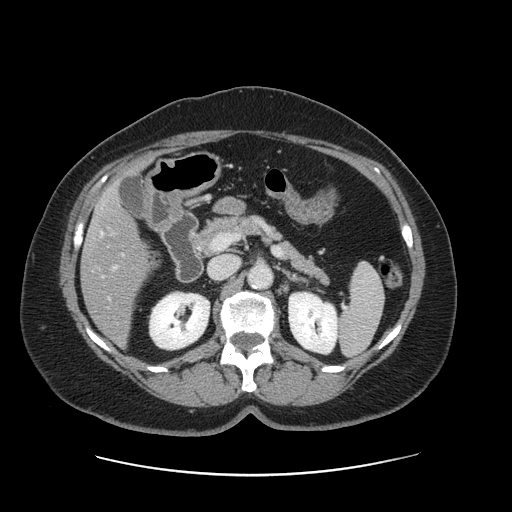
Contrast-enhanced abdominal CT, one axial slice; slice 70 of 161 in the series (ordered by position); intravenous contrast given; soft-tissue window (W 400 / L 40 HU); 2.5 mm slice thickness; 512 × 512 image matrix, field of view 398 × 398 mm. Female patient, age 62 years. From the clinical record (not read from this slice): diagnosis: colorectal cancer liver metastases, imaged before liver resection; multiple liver metastases: no; largest metastasis: 2.5 cm; disease in both lobes: no.
Structures marked on this image (manually delineated by an expert):
- hepatic veins: bounding box (x1, y1, x2, y2) in pixels: (101, 232, 110, 299)
- liver: (82, 187, 151, 345)
- portal vein (with intrahepatic branches): (111, 232, 116, 268)